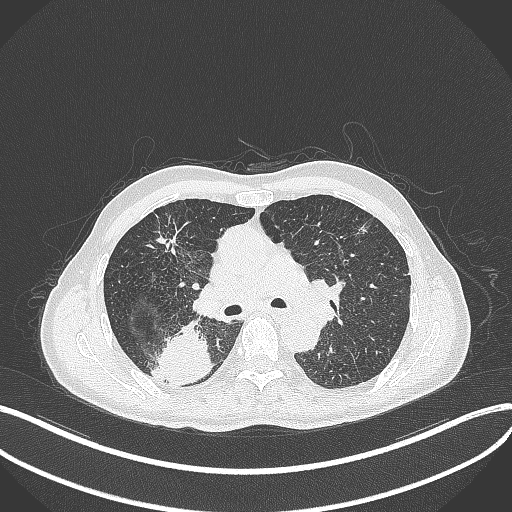
Chest CT, one axial slice. Slice 279 of 428 in the series (ordered by position). Reconstruction kernel B70f. Lung window (W 1500 / L -600 HU). 1 mm slice thickness. 512 × 512 image matrix, field of view 400 × 400 mm. Male patient, age 79 years. Case-level facts recorded for this patient, not image findings: clinical TNM (as recorded): T3 N0 M0.
Annotated regions visible in this slice (bounding box drawn by a radiologist):
- lung tumour (recorded histology: adenocarcinoma): bounding box <154,317,211,388> (left, top, right, bottom; pixels)